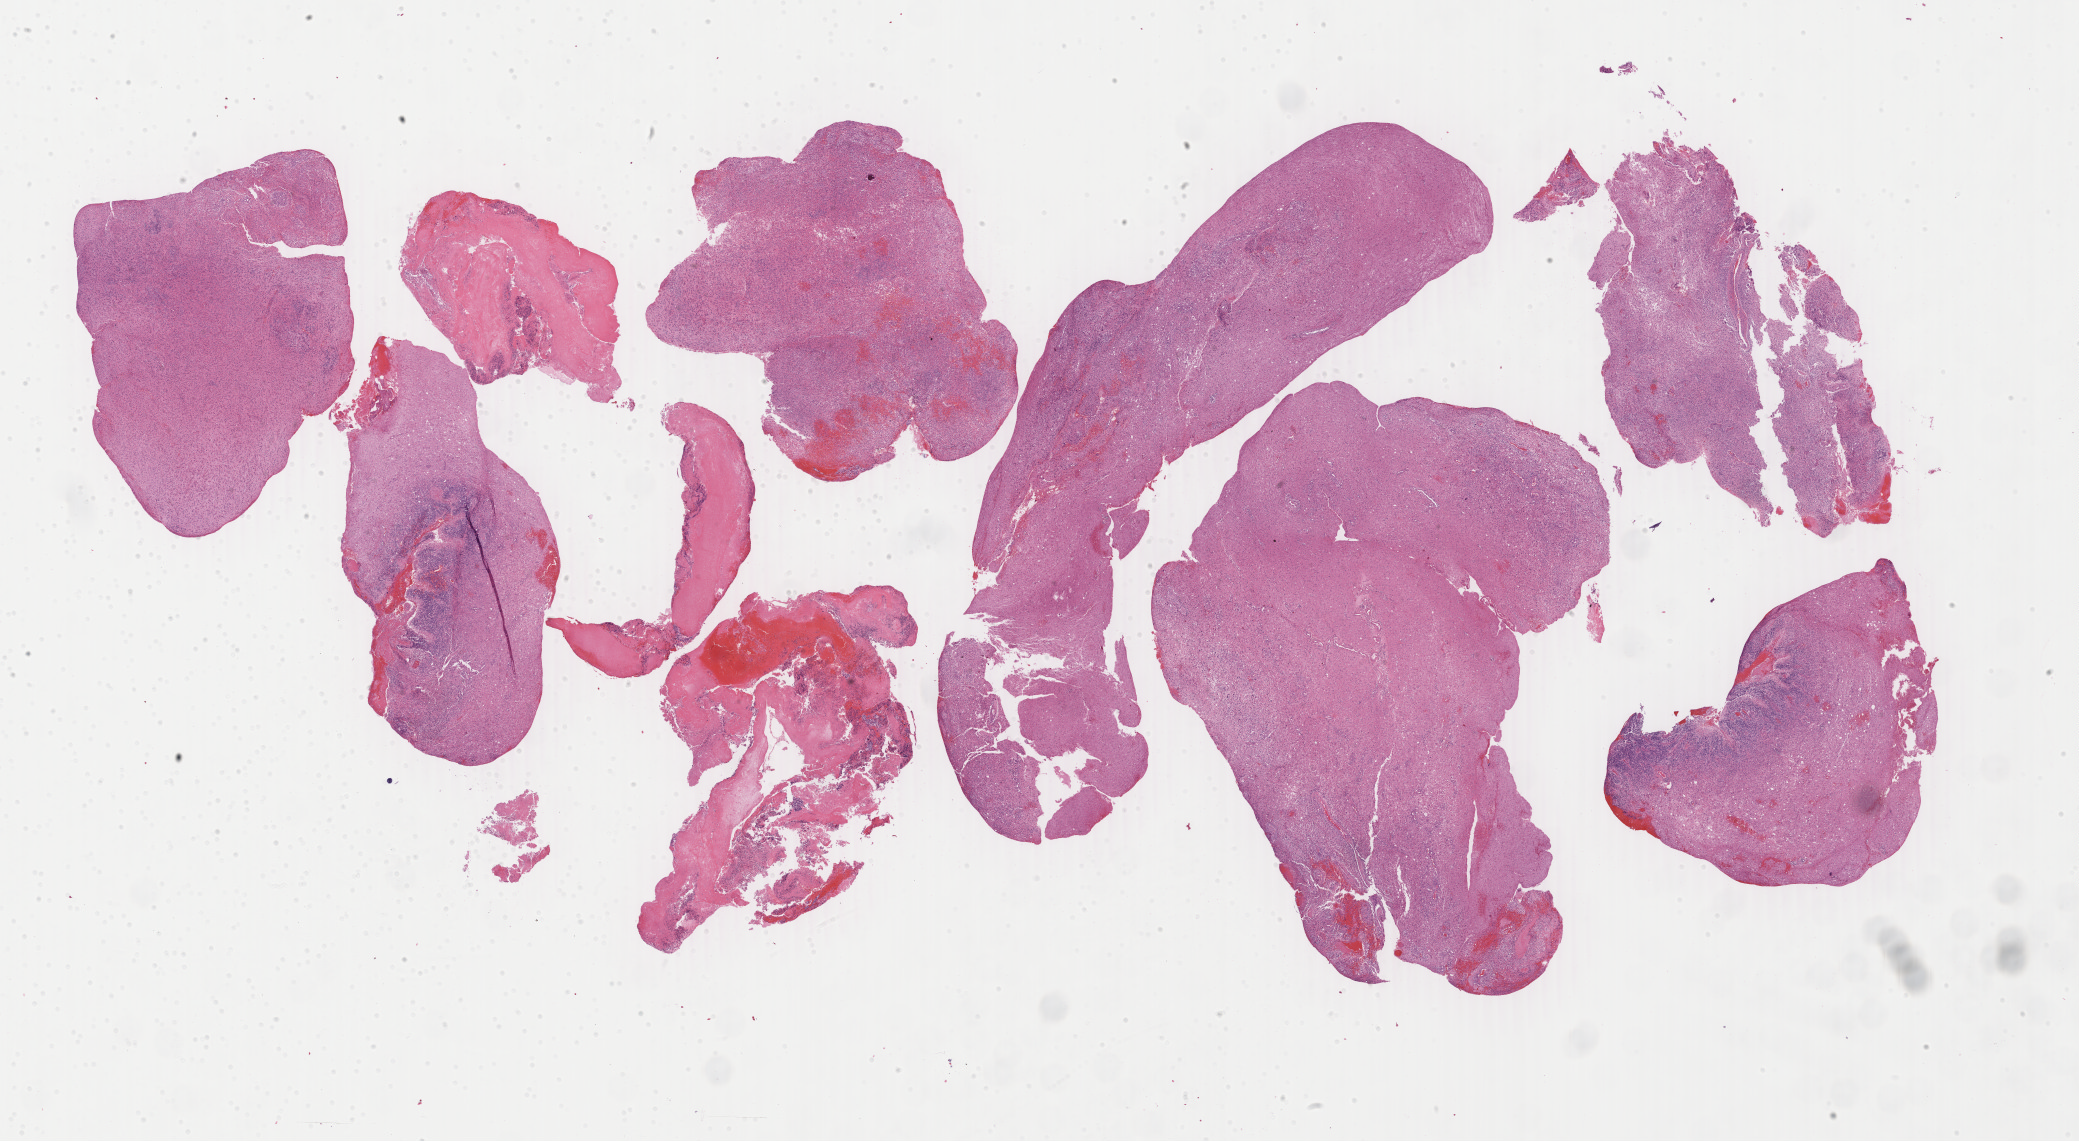
H&E whole-slide image — low-resolution overview of the scanned area, about 33.1 x 18.2 mm (acquisition: 40x scan); formalin-fixed paraffin-embedded (FFPE) diagnostic section; brain, primary tumour sample. Female patient; age at initial diagnosis 78 years.
Diagnosis: Glioblastoma.